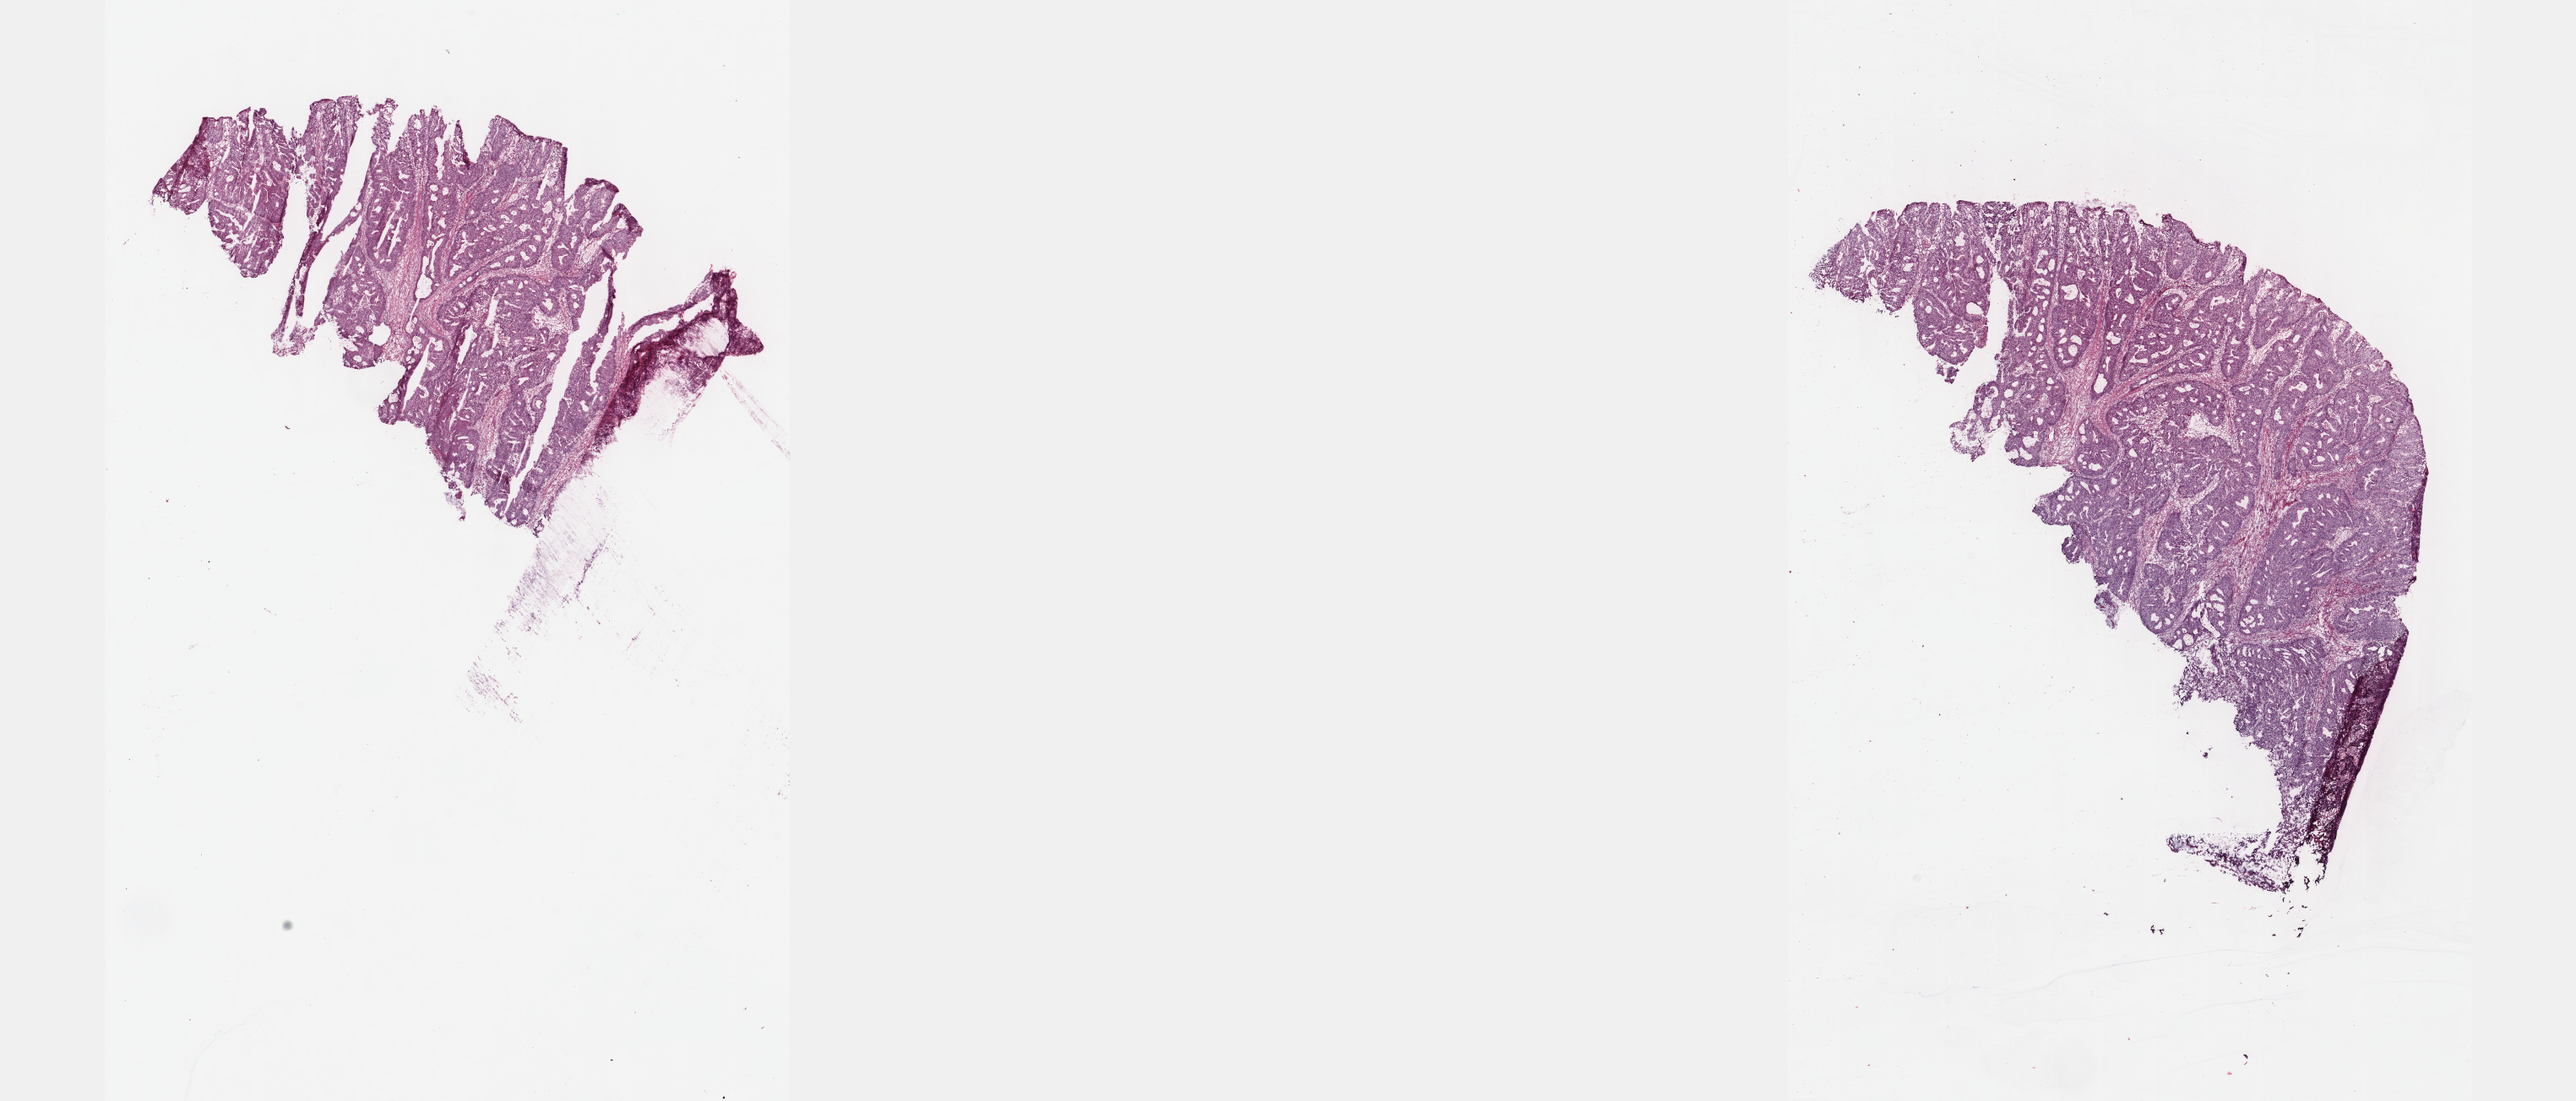
Whole-slide histology image, H&E-stained, a low-resolution overview of the entire scanned area, about 24.6 x 10.5 mm; frozen section; rectum, primary tumour sample. Patient: female, age at initial diagnosis 62 years. Slide review estimates, as recorded: tumour cells 85%, tumour nuclei 90%.
Pathologic diagnosis: Adenocarcinoma, NOS.